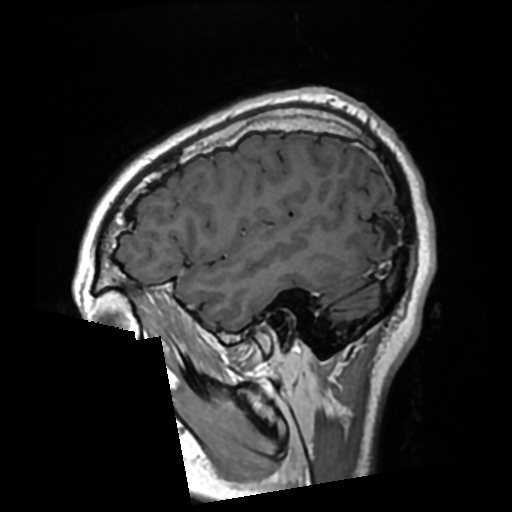
Brain MRI from a brain-tumour surgery series, one sagittal slice. Position 73 of 276 along the scan axis. T1-weighted post-contrast. 0.7 mm slice thickness. 512 × 512 image matrix, field of view 250 × 250 mm. From the clinical record (not read from this slice): histopathology: Glioma with ependymal features; WHO grade: 2; tumour location: Left Parietal.
Outlined on this slice (expert manual segmentation):
- previous resection cavity: box from (x=379, y=227) to (x=393, y=247) px